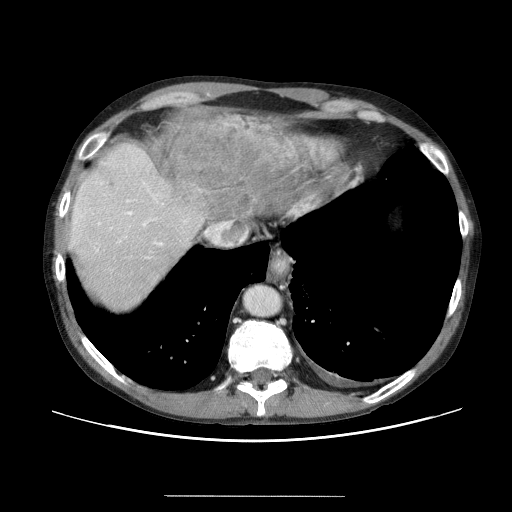
Contrast-enhanced abdominal CT (liver protocol), one axial slice. Slice 54 of 69 in the series (ordered by position). Reconstruction kernel STANDARD. 120 kVp. Soft-tissue window (W 400 / L 40 HU). 2.5 mm slice thickness. 512 × 512 image matrix, field of view 380 × 380 mm. Case-level facts recorded for this patient, not image findings: diagnosis: hepatocellular carcinoma (patient treated with transarterial chemoembolisation; whether this scan precedes or follows treatment is not stated here); TNM stage (as recorded): Stage-IVB; Child-Pugh class: B.
Structures marked on this image (semi-automatically segmented with operator editing):
- liver parenchyma outside the tumour (the mass and vessels are separate outlines, so this box may not span the whole liver): bounding box (x1, y1, x2, y2) in pixels: (66, 113, 324, 322)
- mass: (158, 113, 323, 246)
- liver vessels: (99, 173, 143, 271)